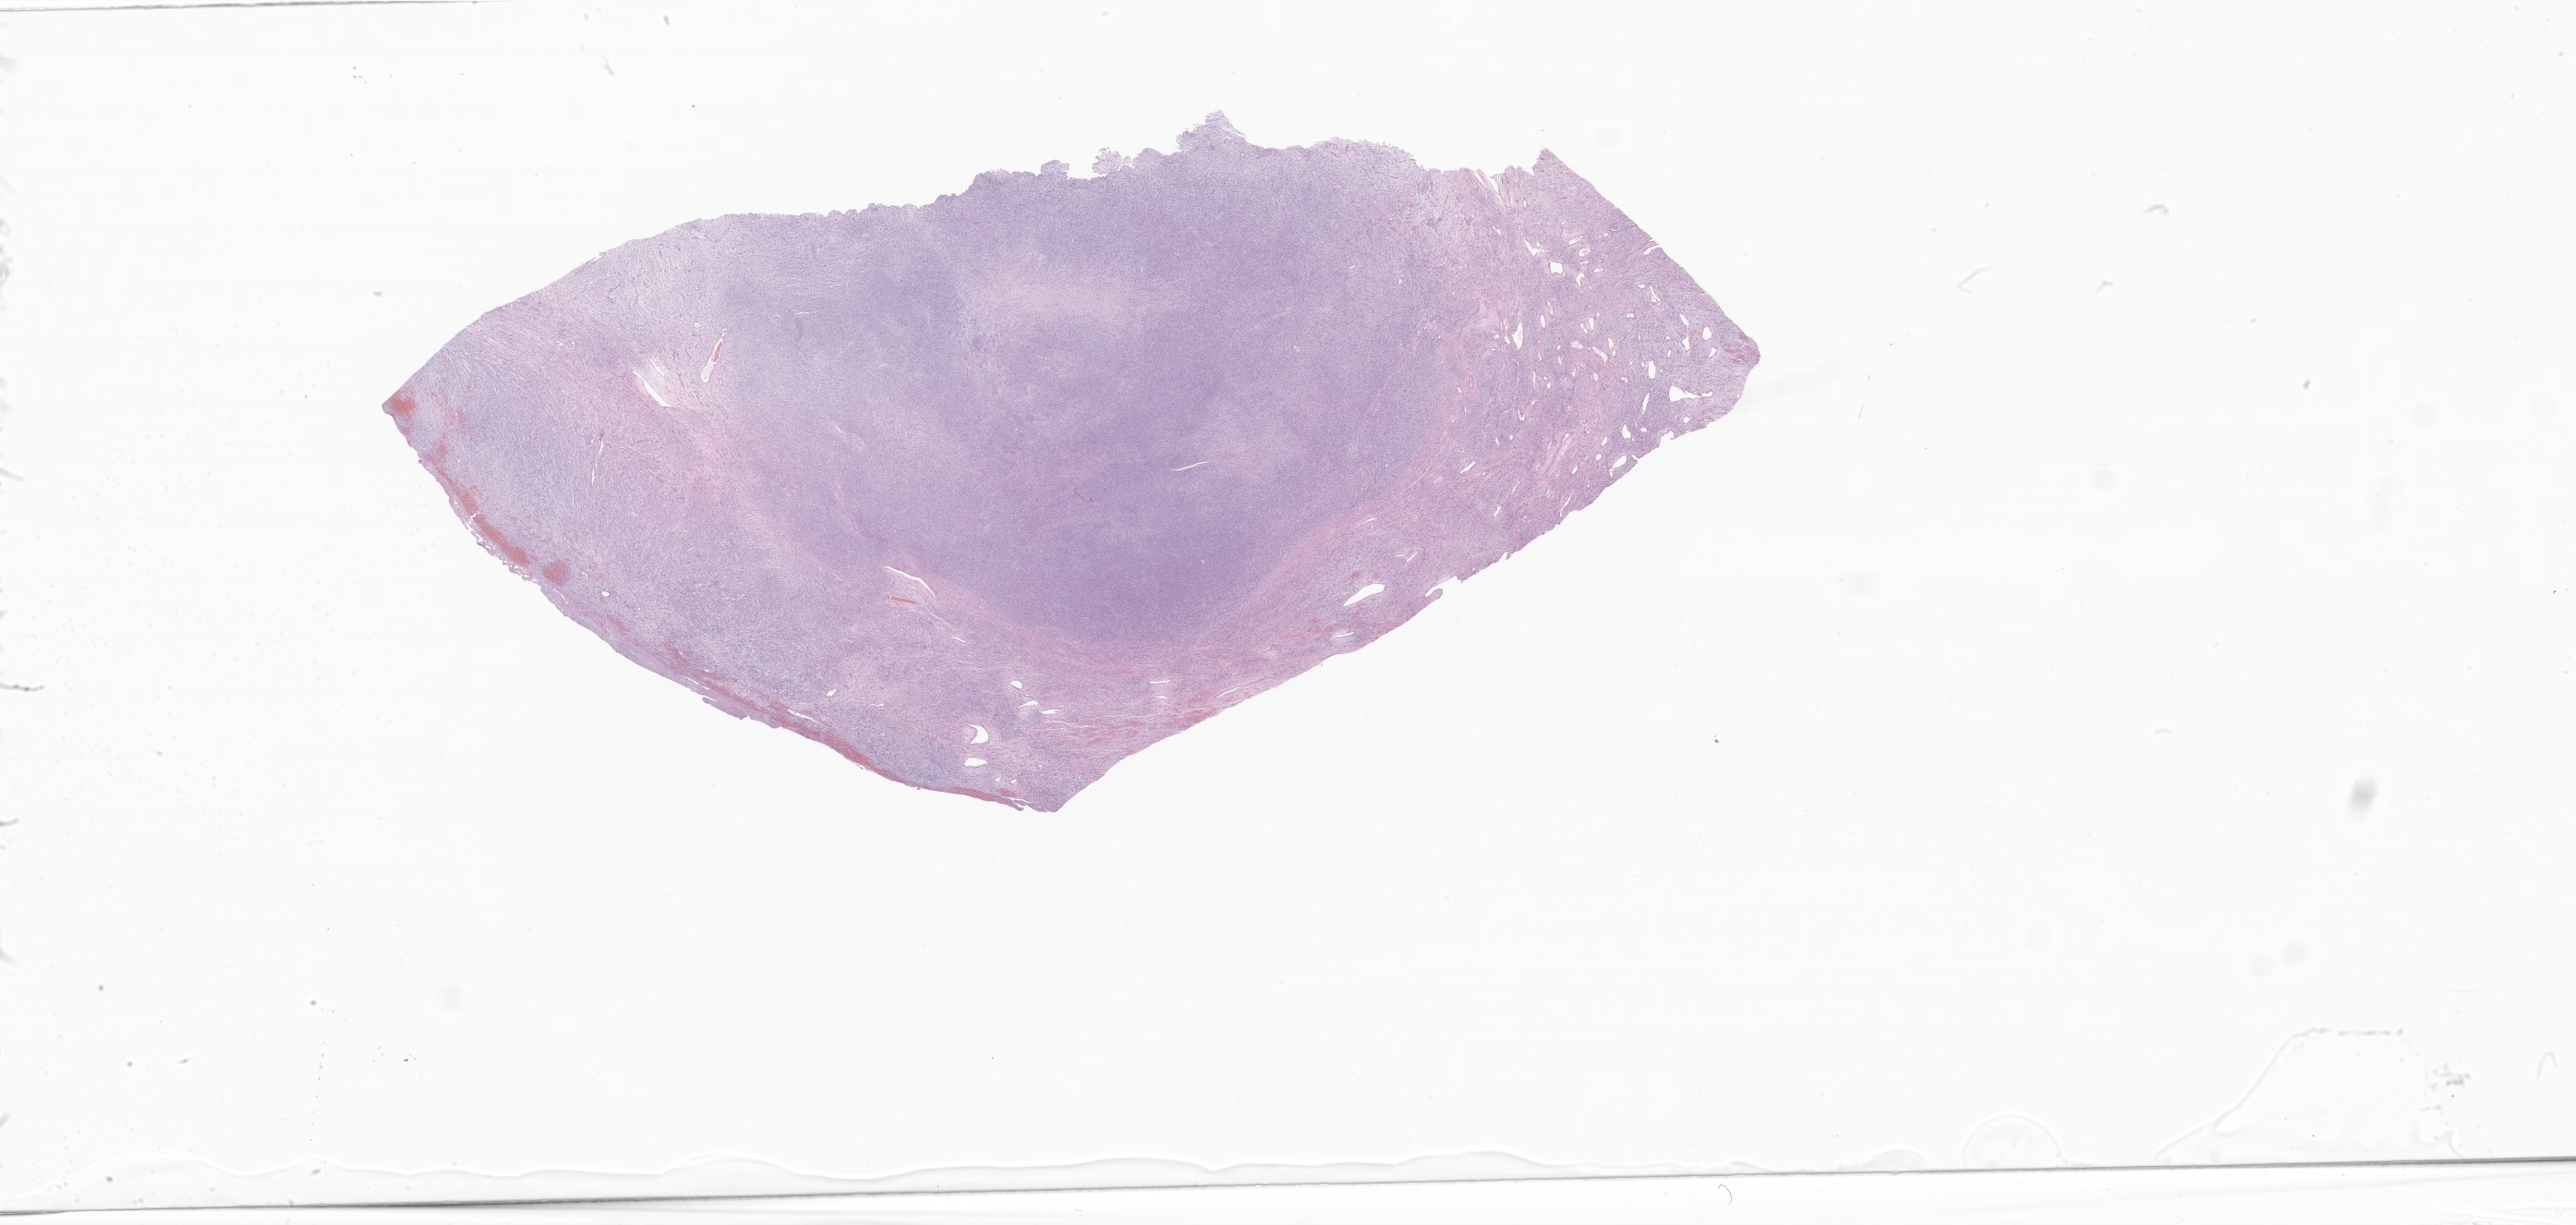
Digitized hematoxylin and eosin (H&E)-stained section of tumor tissue from the testis, whole scanned area (about 47.0 x 22.4 mm) shown as a low-resolution overview, formalin-fixed, paraffin-embedded (FFPE) tissue. Patient: male, age 179 months (14 years 11 months).
Diagnosis (ICD-O-3 morphology term): Rhabdomyosarcoma, NOS.